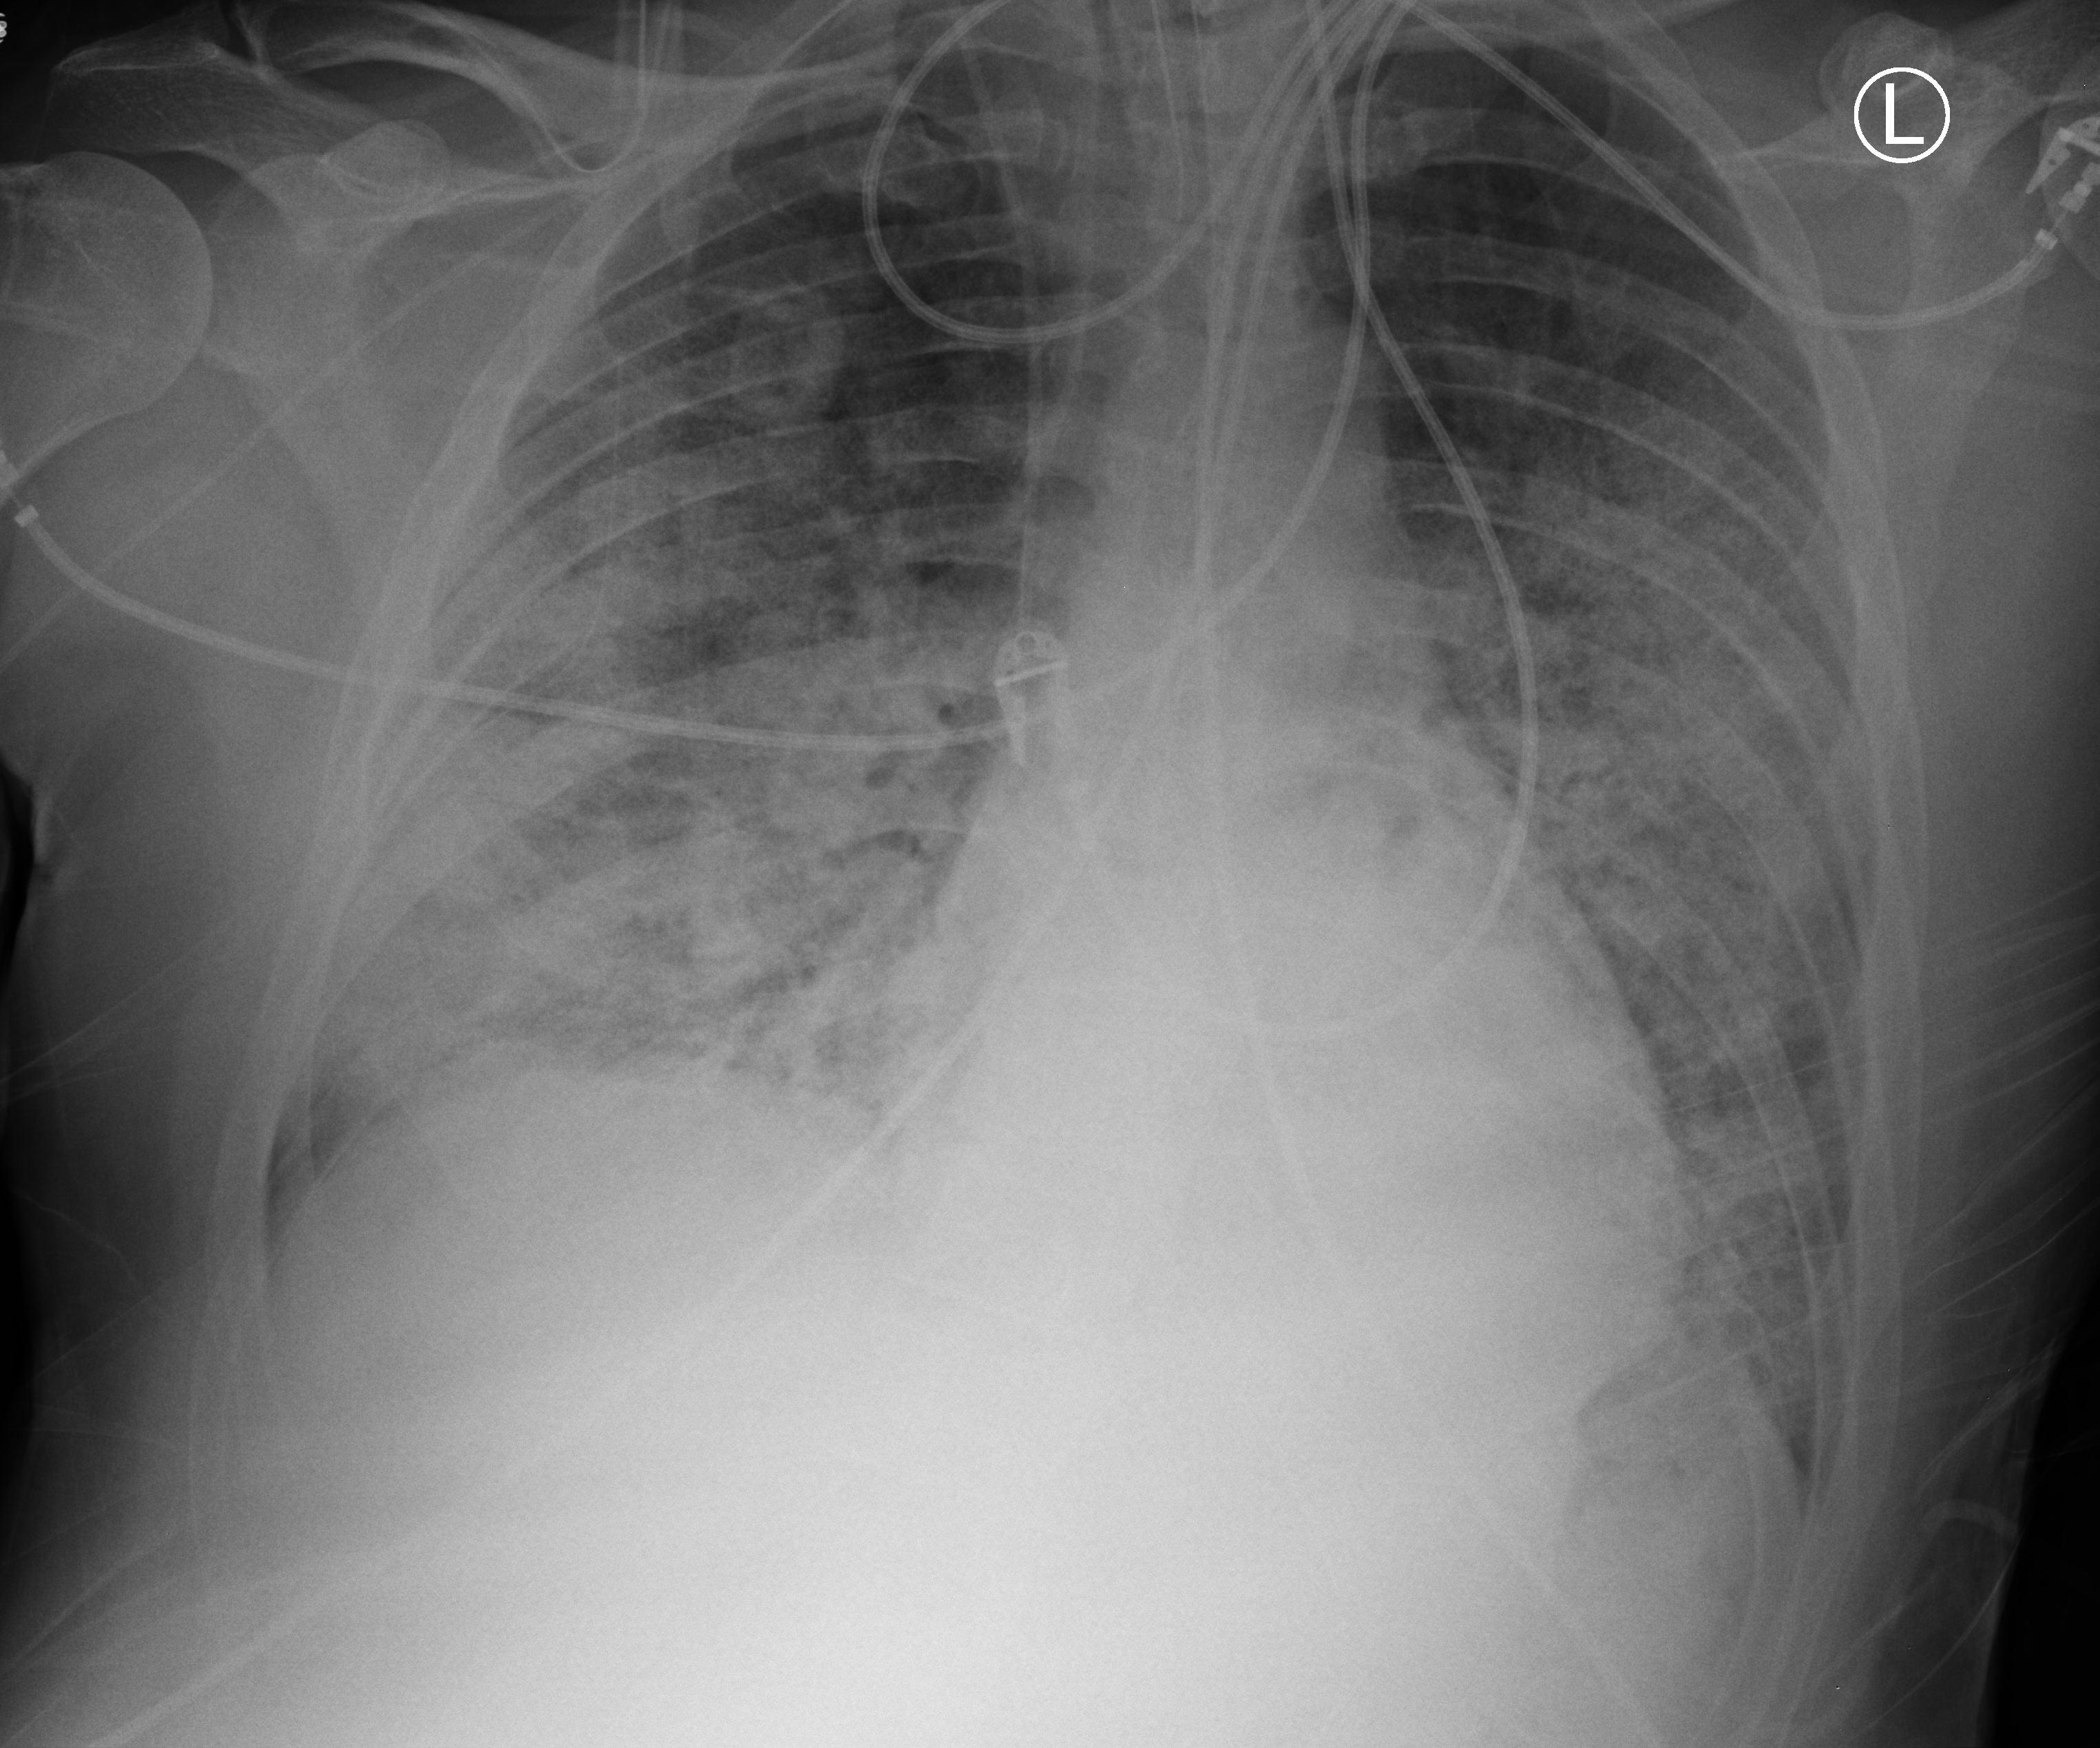
Portable chest radiograph, anteroposterior (AP) projection. Male patient hospitalised with COVID-19, age 18–59 years.
Hospital-stay facts (about this admission, not read from this image; timing relative to this image not recorded): mechanically ventilated during this hospital stay: yes.